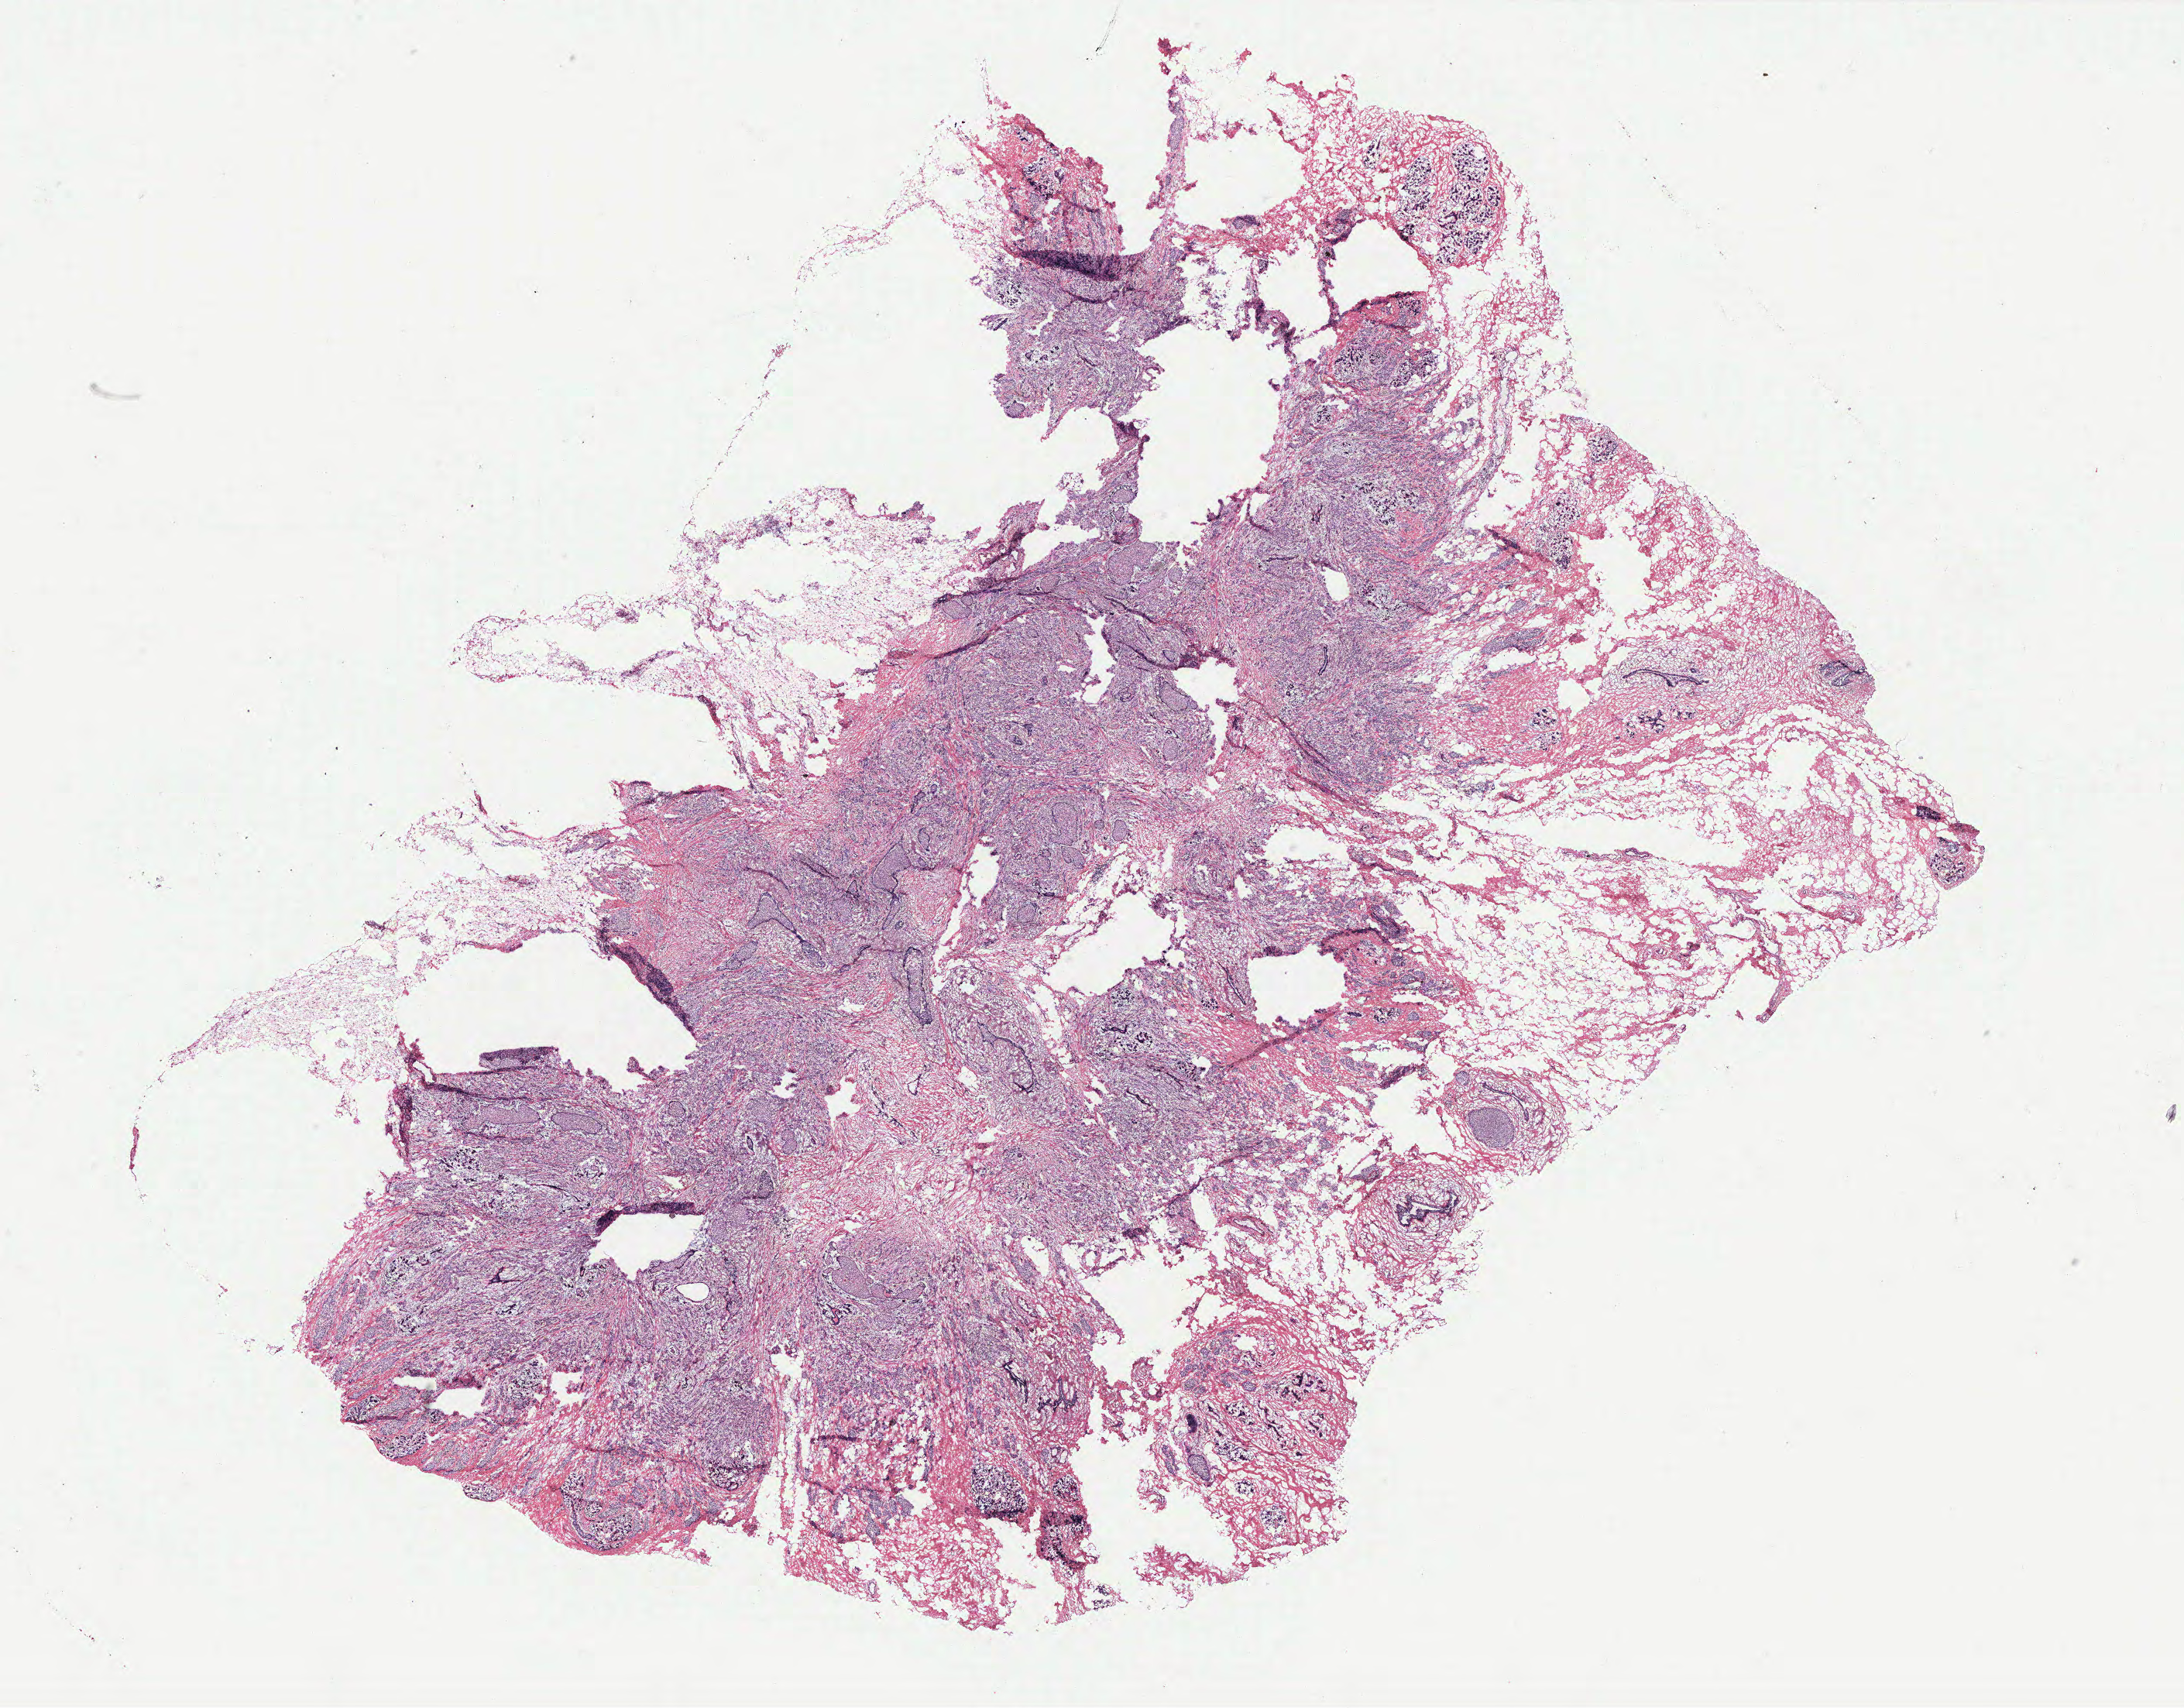
Digitized H&E tissue section (whole slide), a low-resolution overview of the entire scanned area, about 22.6 x 17.7 mm (from a 40x scan); breast, tissue type not recorded. 49-year-old female patient.
• patient diagnosis: Infiltrating lobular carcinoma, NOS